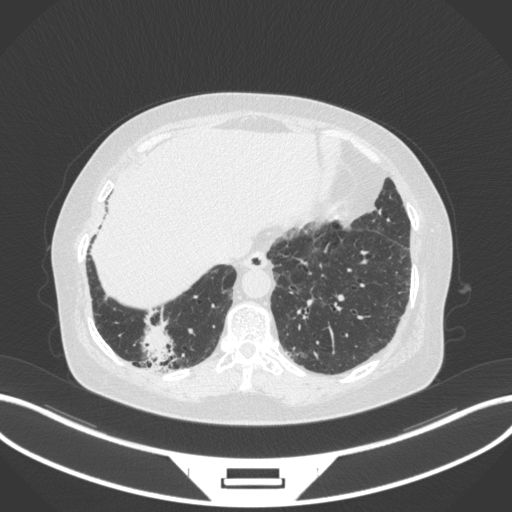
Chest CT, one axial slice. Position 30 of 303 along the scan axis. 120 kVp. Lung window (W 1500 / L -600 HU). 1 mm slice thickness. 512 × 512 image matrix, field of view 400 × 400 mm. Patient: female, 65 years. Case-level facts recorded for this patient, not image findings: clinical TNM (as recorded): T2b N1 M0; histopathological grade: G1.
Annotated regions visible in this slice (bounding box drawn by a radiologist):
- lung tumour (recorded histology: adenocarcinoma): bounding box [x1, y1, x2, y2] px = [139, 323, 176, 369]